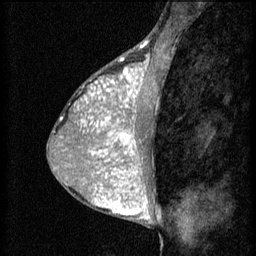
Breast MRI (dynamic contrast-enhanced), one sagittal slice. Position 30 of 60 along the scan axis. 3 images stored at this slice position (order not interpretable as contrast timing). 1.5 T. TE 4.2 ms, TR 8.2 ms. 2 mm slice thickness. 256 × 256 image matrix. Female patient, age 38 years.
Structures marked on this image (semi-automatically segmented with operator editing):
- analysis volume of interest (the breast-tissue region the enhancement analysis was run in; not a lesion): bounding box <95,106,153,171> (left, top, right, bottom; pixels)
- tumour enhancement mask (voxels above the 70 % enhancement threshold inside the analysis volume of interest): <96,106,142,171>